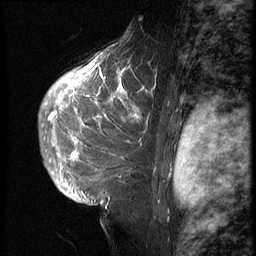
Breast MRI (dynamic contrast-enhanced), one sagittal slice. 3 images stored at this slice position (order not interpretable as contrast timing). 1.5 T. TE 4.2 ms, TR 9 ms. 2.5 mm slice thickness. 256 × 256 image matrix. Female patient, age 28 years. From the clinical record (not read from this slice): setting: breast cancer imaged before/during neoadjuvant chemotherapy.
Outlined on this slice (semi-automatic segmentation, software-assisted and operator-edited):
- analysis volume of interest (the breast-tissue region the enhancement analysis was run in; not a lesion): bounding box <42,45,158,207> (left, top, right, bottom; pixels)
- tumour enhancement mask (voxels above the 140 % enhancement threshold inside the analysis volume of interest): <48,66,153,200>